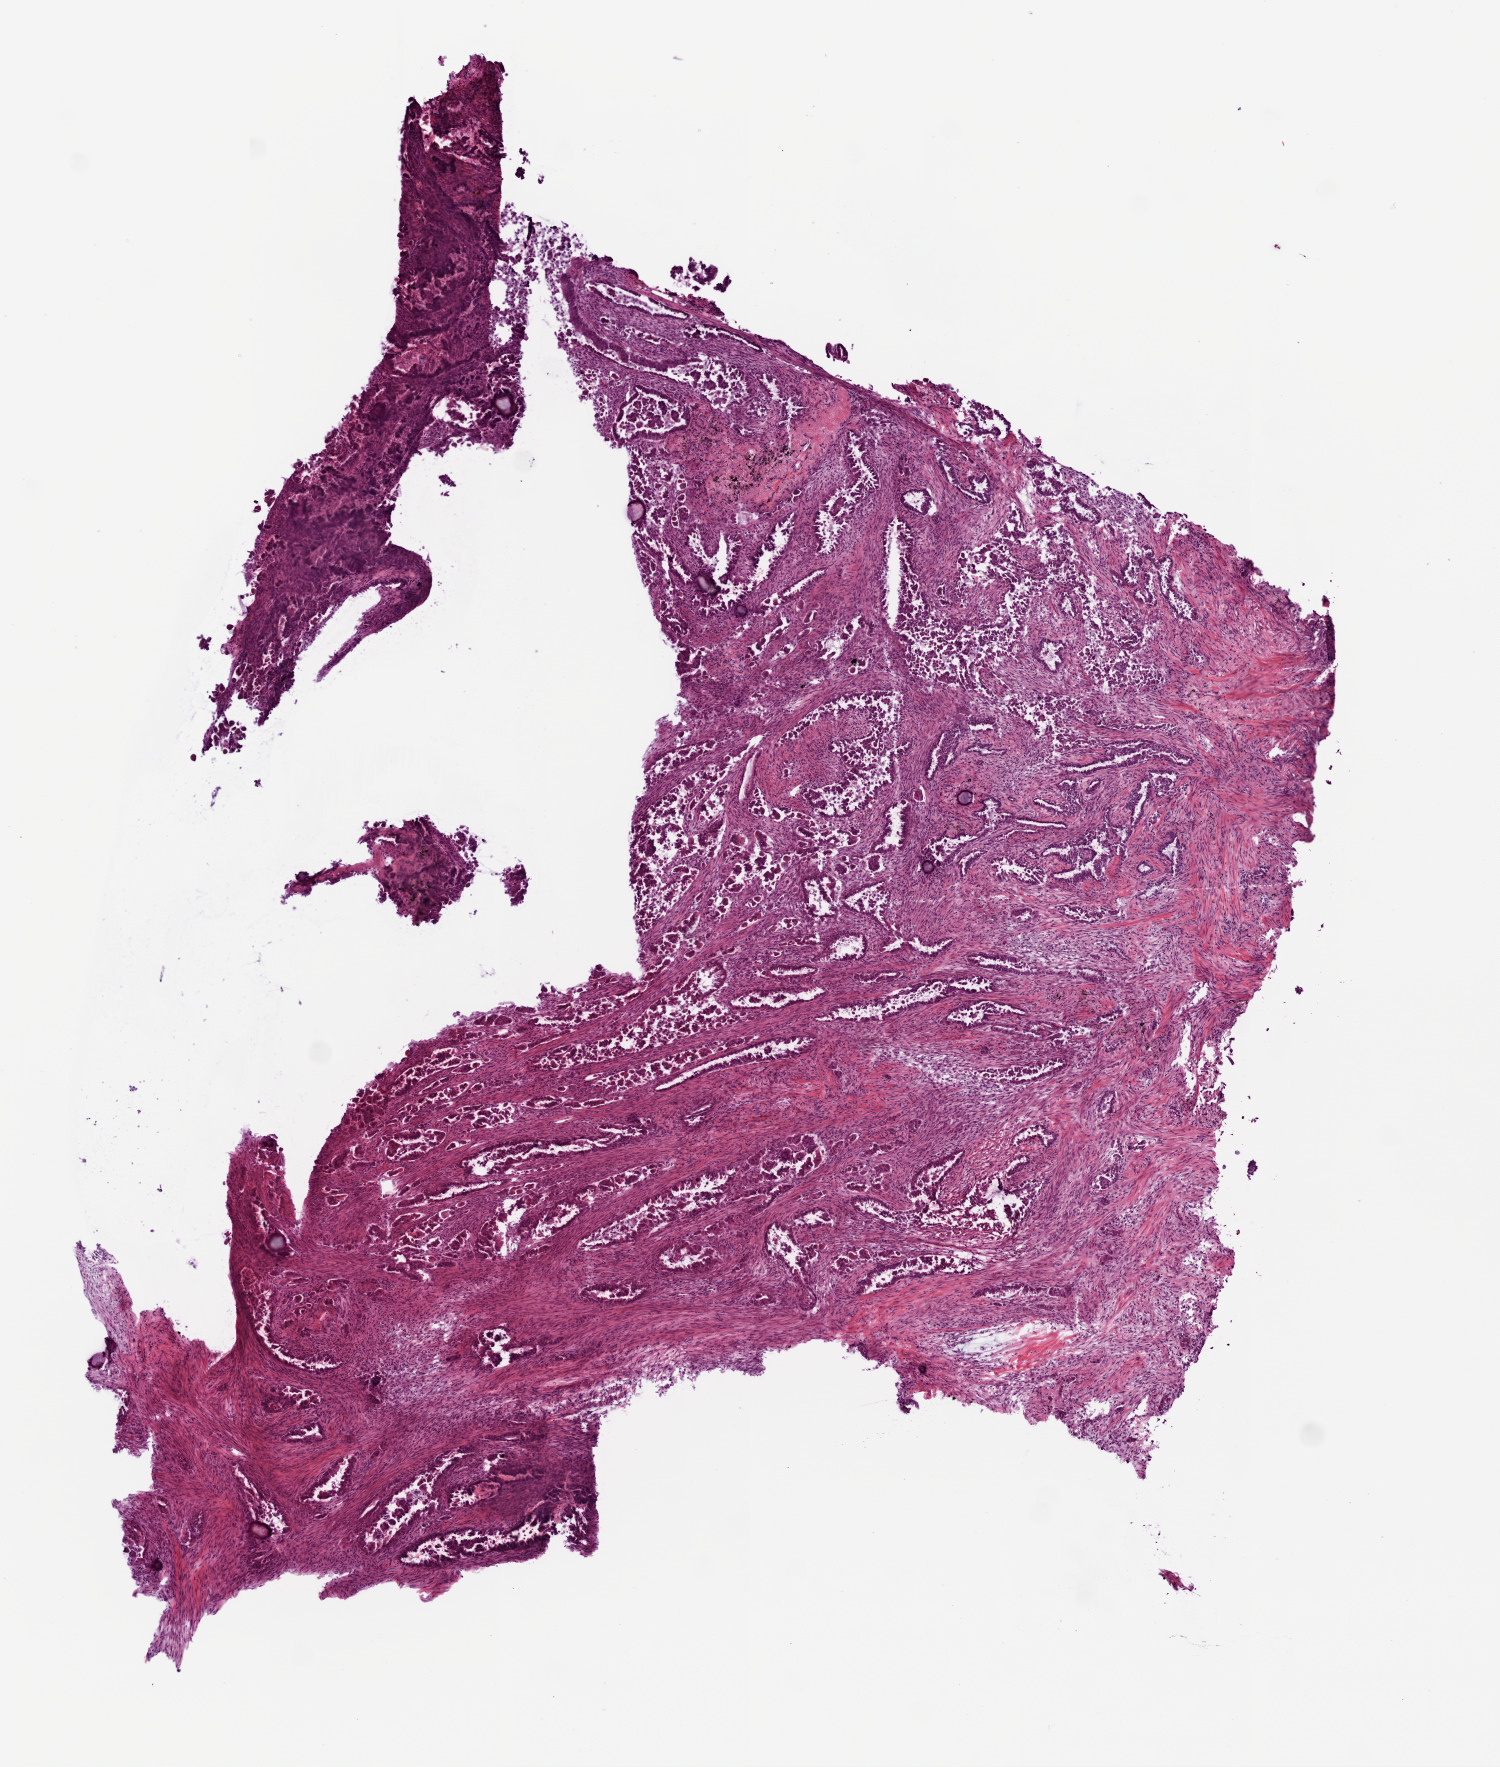
Whole-slide histology image, H&E-stained — shown as a low-resolution overview of the whole scanned area (about 6.0 x 7.1 mm, slide scanned at 20x). Frozen section. Primary tumour sample from the lung. Female patient; age at initial diagnosis 78 years.
Histologic diagnosis: Acinar cell carcinoma.